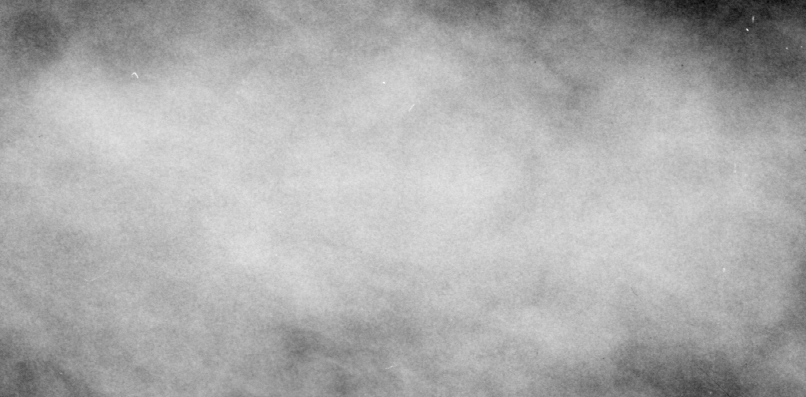
Cropped region of a digitized screen-film mammogram centred on a radiologist-marked abnormality; left breast; MLO view.
Mass, shape lobulated / irregular, margins obscured / ill defined; BI-RADS assessment category 4; subtlety rating 4 on a 1 (subtle) to 5 (obvious) scale; pathology result (as recorded, not read from the image): malignant.